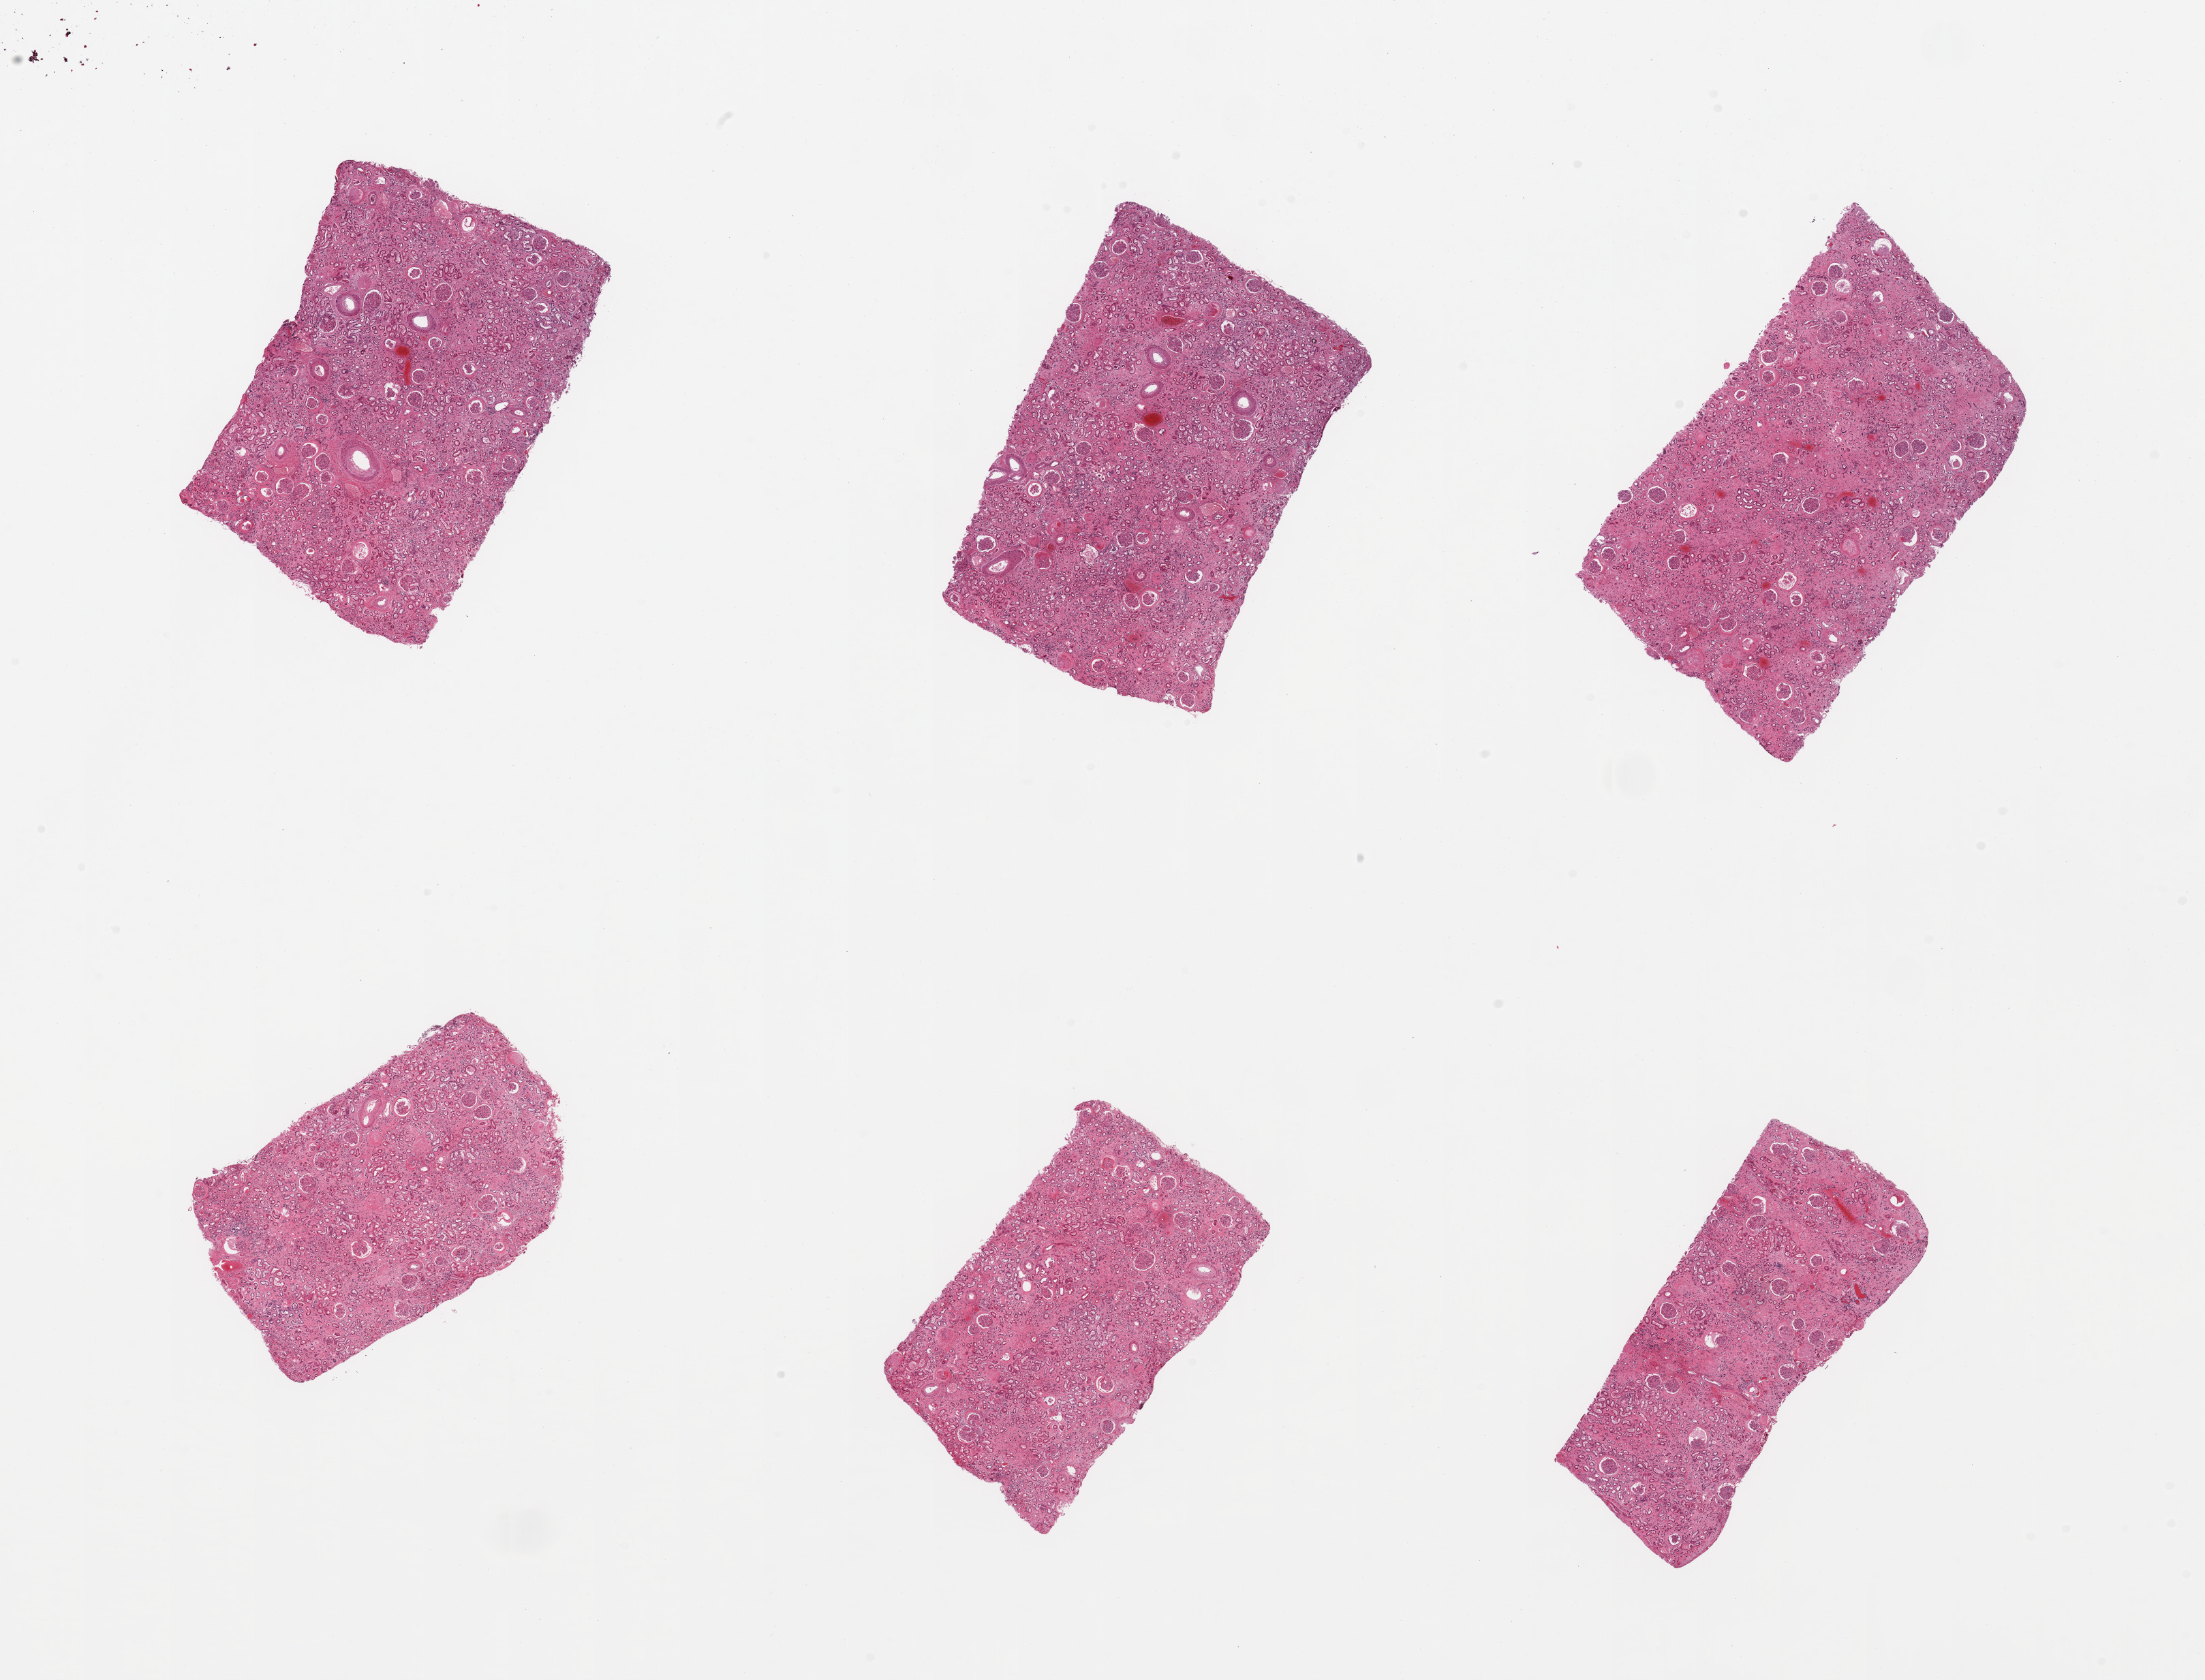
H&E whole-slide image, brightfield, low-resolution overview of the scanned area, about 25.6 x 19.5 mm; PAXgene-fixed, paraffin-embedded tissue; sampled site (target tissue): renal cortex; tissue donor sample. Donor sex: male.
- reviewer comment on this tissue sample: 6 pieces, glomeruli present, prominent mesangium with 'wire loops', prominent interstitial hyalinization, moderate tubular autolysis